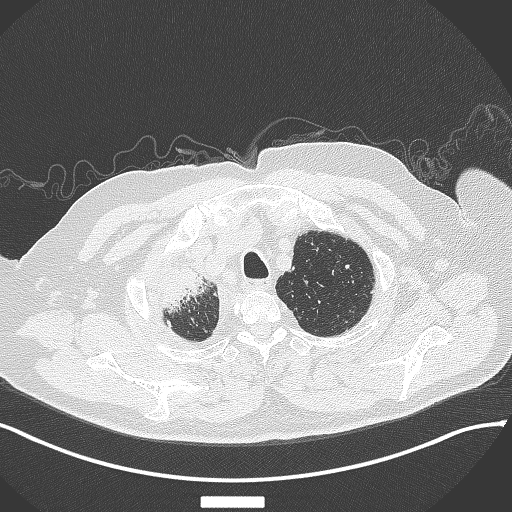
Chest CT, one axial slice; reconstruction kernel B70f; lung window (W 1500 / L -600 HU); 1 mm slice thickness; 512 × 512 image matrix. Male patient, age 69 years. From the clinical record (not read from this slice): clinical TNM (as recorded): T4 N3 M1.
Outlined on this slice (bounding box drawn by a radiologist):
- lung tumour (recorded histology: adenocarcinoma): box from (x=152, y=261) to (x=218, y=313) px